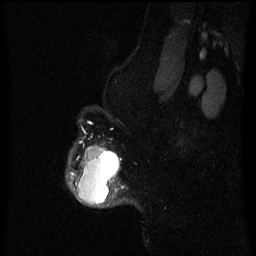
Breast MRI (dynamic contrast-enhanced), one sagittal slice; position 54 of 60 along the scan axis; dynamic contrast-enhanced series, image 2 of 3 at this slice position (ordered by acquisition); 1.5 T; TE 4.2 ms, TR 8 ms; 256 × 256 image matrix, field of view 190 × 190 mm. Patient: female, 50 years.
Structures marked on this image (semi-automatic segmentation, software-assisted and operator-edited):
- analysis volume of interest (the breast-tissue region the enhancement analysis was run in; not a lesion): bounding box (x1, y1, x2, y2) in pixels: (67, 146, 124, 208)
- tumour enhancement mask (voxels above the 70 % enhancement threshold inside the analysis volume of interest): (70, 147, 124, 205)